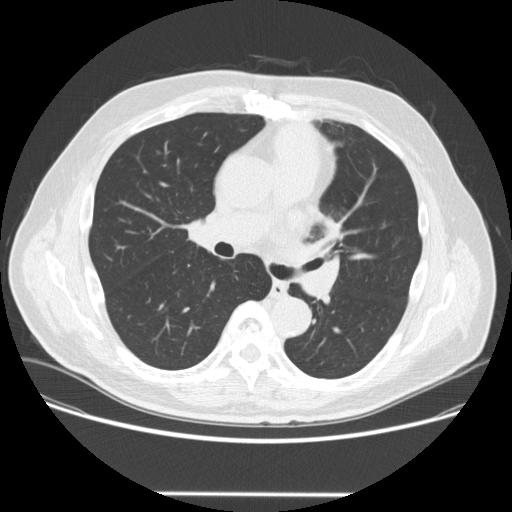
Low-dose screening chest CT, one axial slice; slice 154 of 253 in the series (ordered by position); reconstruction kernel STANDARD; lung window (W 1500 / L -600 HU); 512 × 512 image matrix, field of view 400 × 400 mm.
Annotated regions visible in this slice (expert manual segmentation):
- lesion 1 (tumor, upper lobe of left lung): box from (x=325, y=220) to (x=341, y=239) px